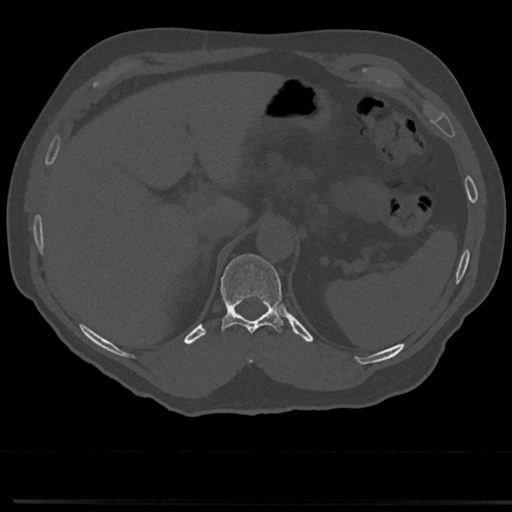
CT including the spine, one axial slice; slice 204 of 817 in the series (ordered by position); 120 kVp; bone window (W 1800 / L 400 HU); 512 × 512 image matrix, field of view 355 × 355 mm. Male patient, age 61 years. From the clinical record (not read from this slice): primary cancer: prostate.
Annotated regions visible in this slice (semi-automatic segmentation, software-assisted and operator-edited):
- T10 vertebra: bounding box <247,350,254,364> (left, top, right, bottom; pixels)
- T11 vertebra: <220,254,284,332>